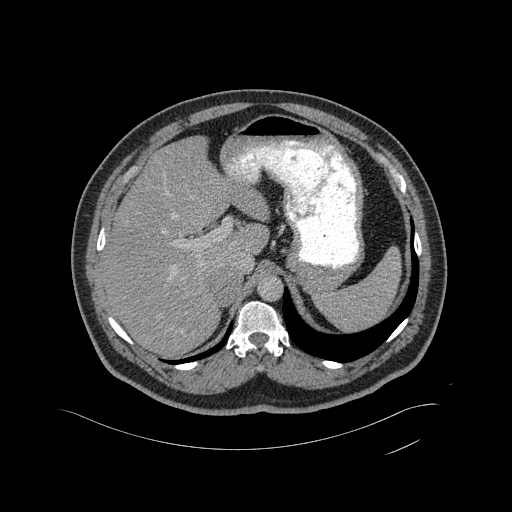
Contrast-enhanced abdominal CT, one axial slice; position 340 of 433 along the scan axis; intravenous contrast given; soft-tissue window (W 400 / L 40 HU); 512 × 512 image matrix, field of view 500 × 500 mm. Male patient, age 56 years. From the clinical record (not read from this slice): diagnosis: adrenocortical carcinoma; tumour side: right adrenal; tumour size at pathology: 11.6 cm; Ki-67 index: 50 %; stage (as recorded): 3.
Annotated regions visible in this slice (semi-automatically segmented with operator editing):
- mass: bounding box [x1, y1, x2, y2] px = [210, 268, 241, 304]